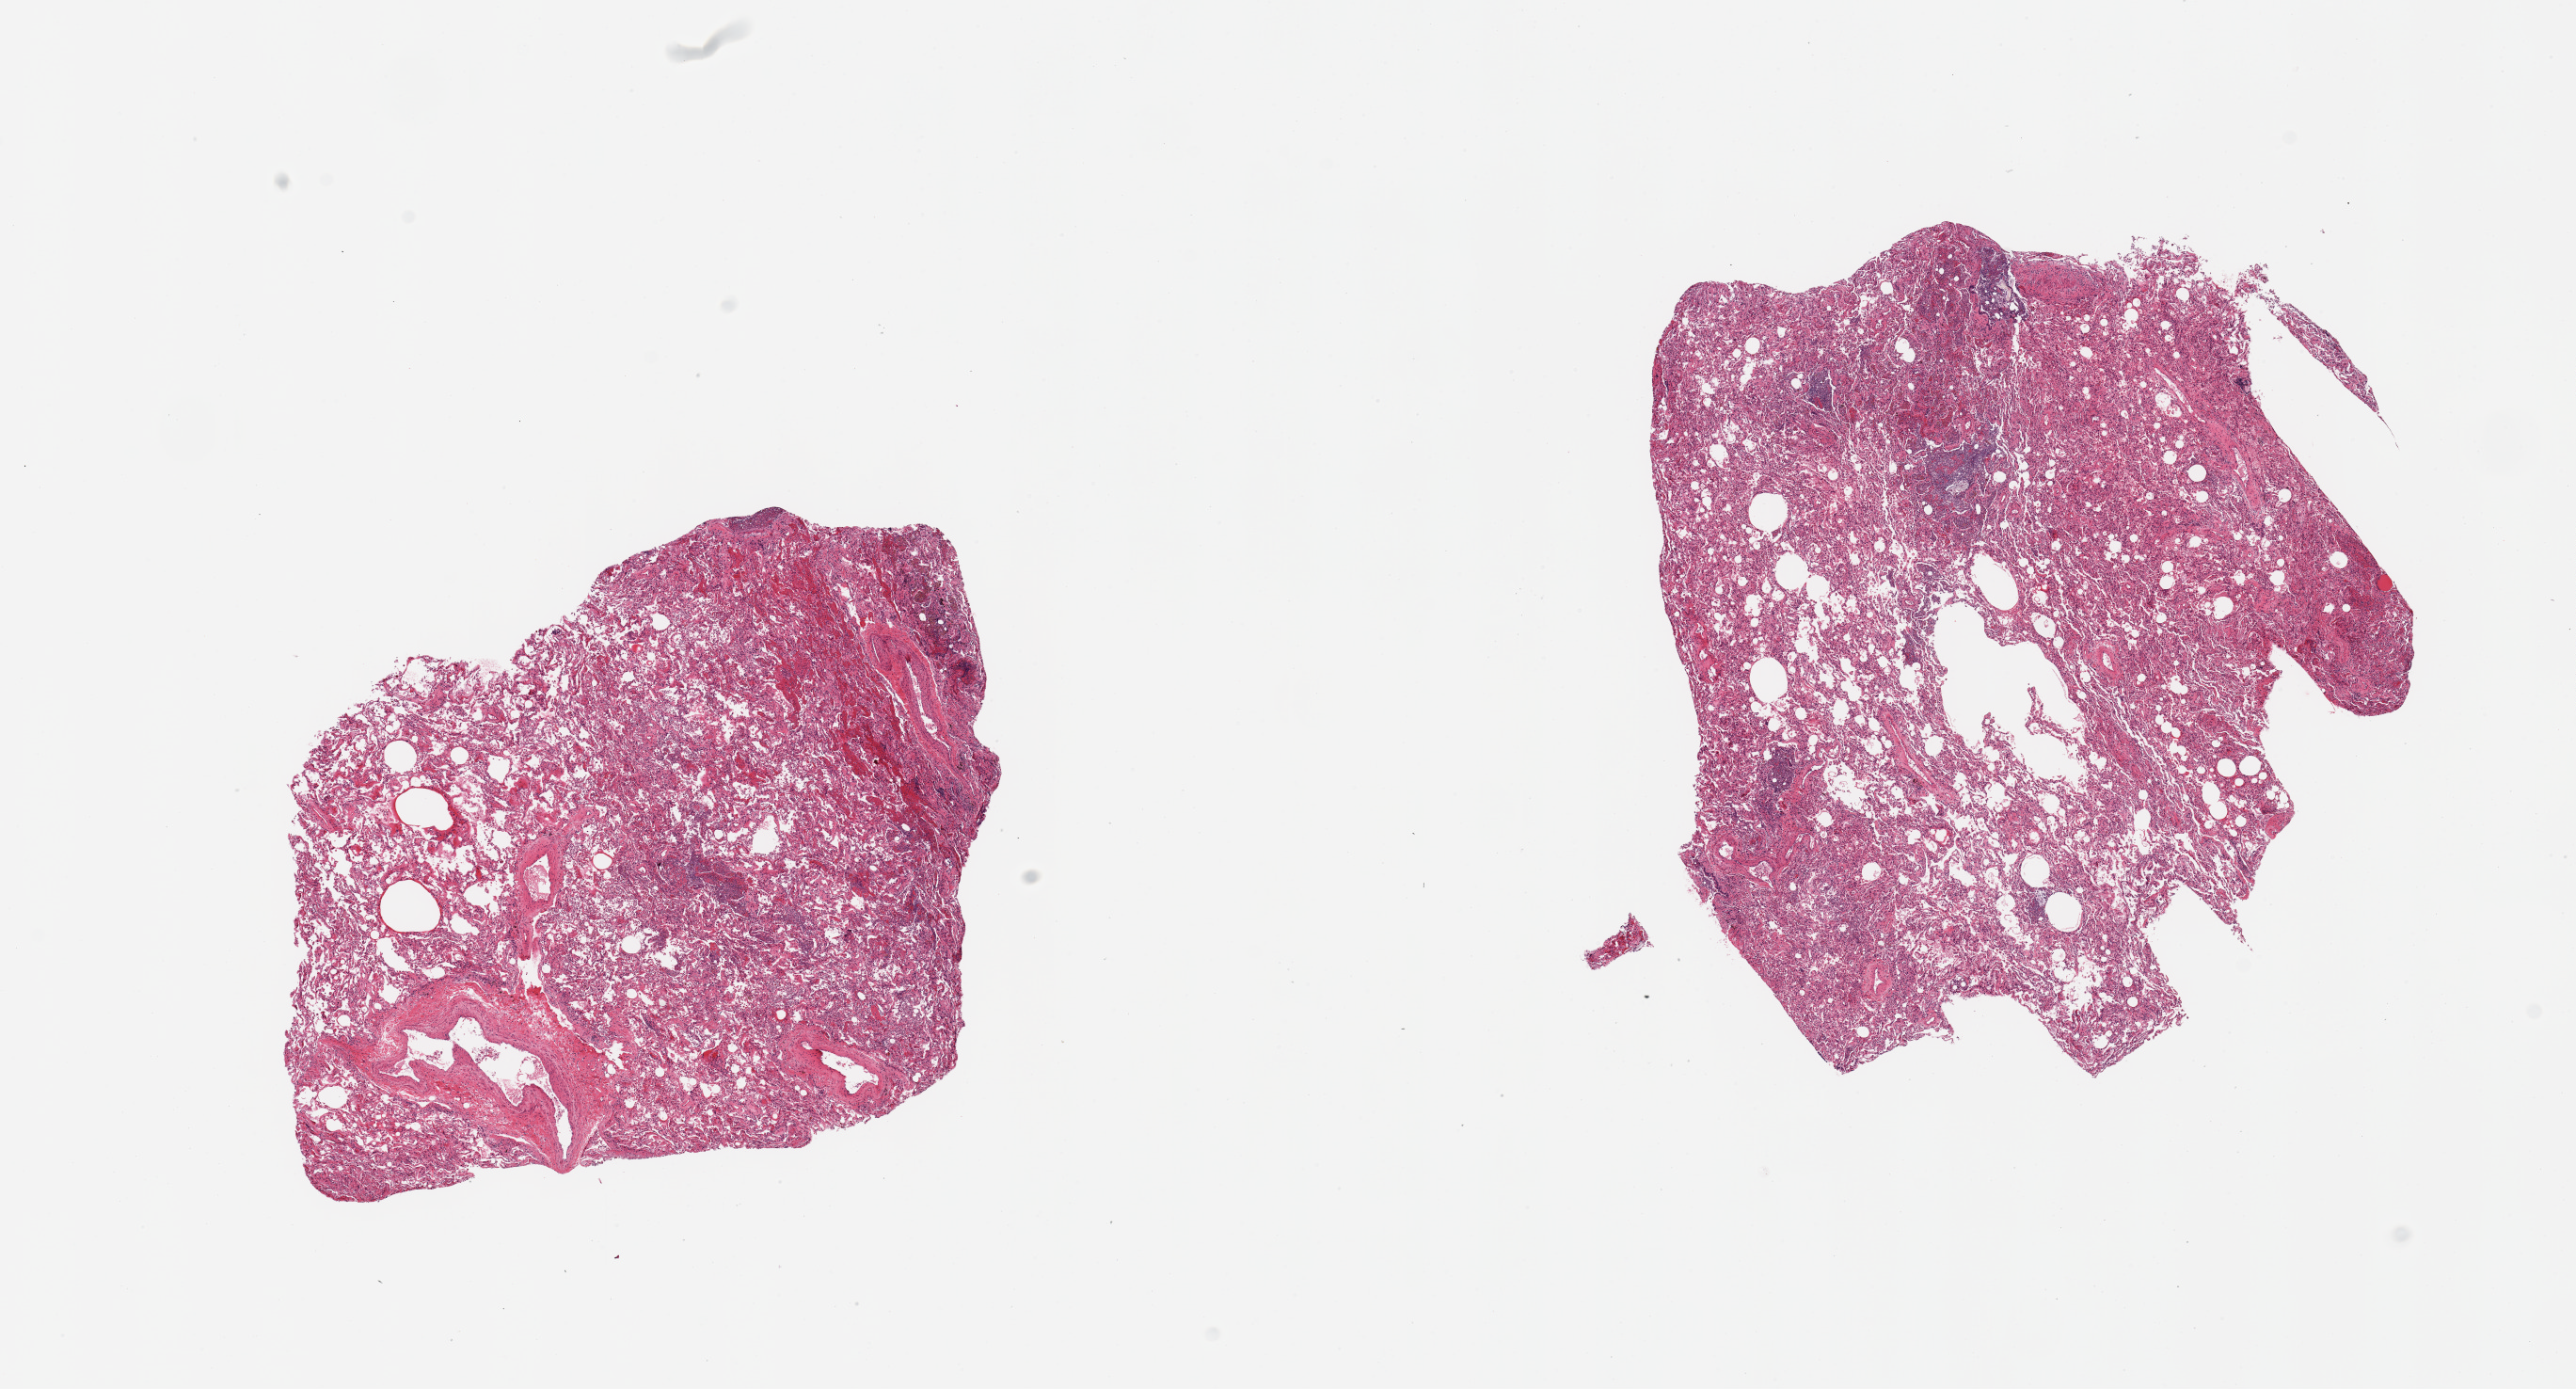
Digitized hematoxylin and eosin (H&E)-stained section — shown as a low-resolution overview of the whole scanned area (about 21.7 x 11.7 mm, from a 20x scan), PAXgene-fixed paraffin-embedded (PFPE) section, section of lung (target tissue), tissue donor sample.
* reviewer comment on this tissue sample: 2 pieces; extensive pneumonia with evidence of aspiration/degenerating animal and vegetable matter